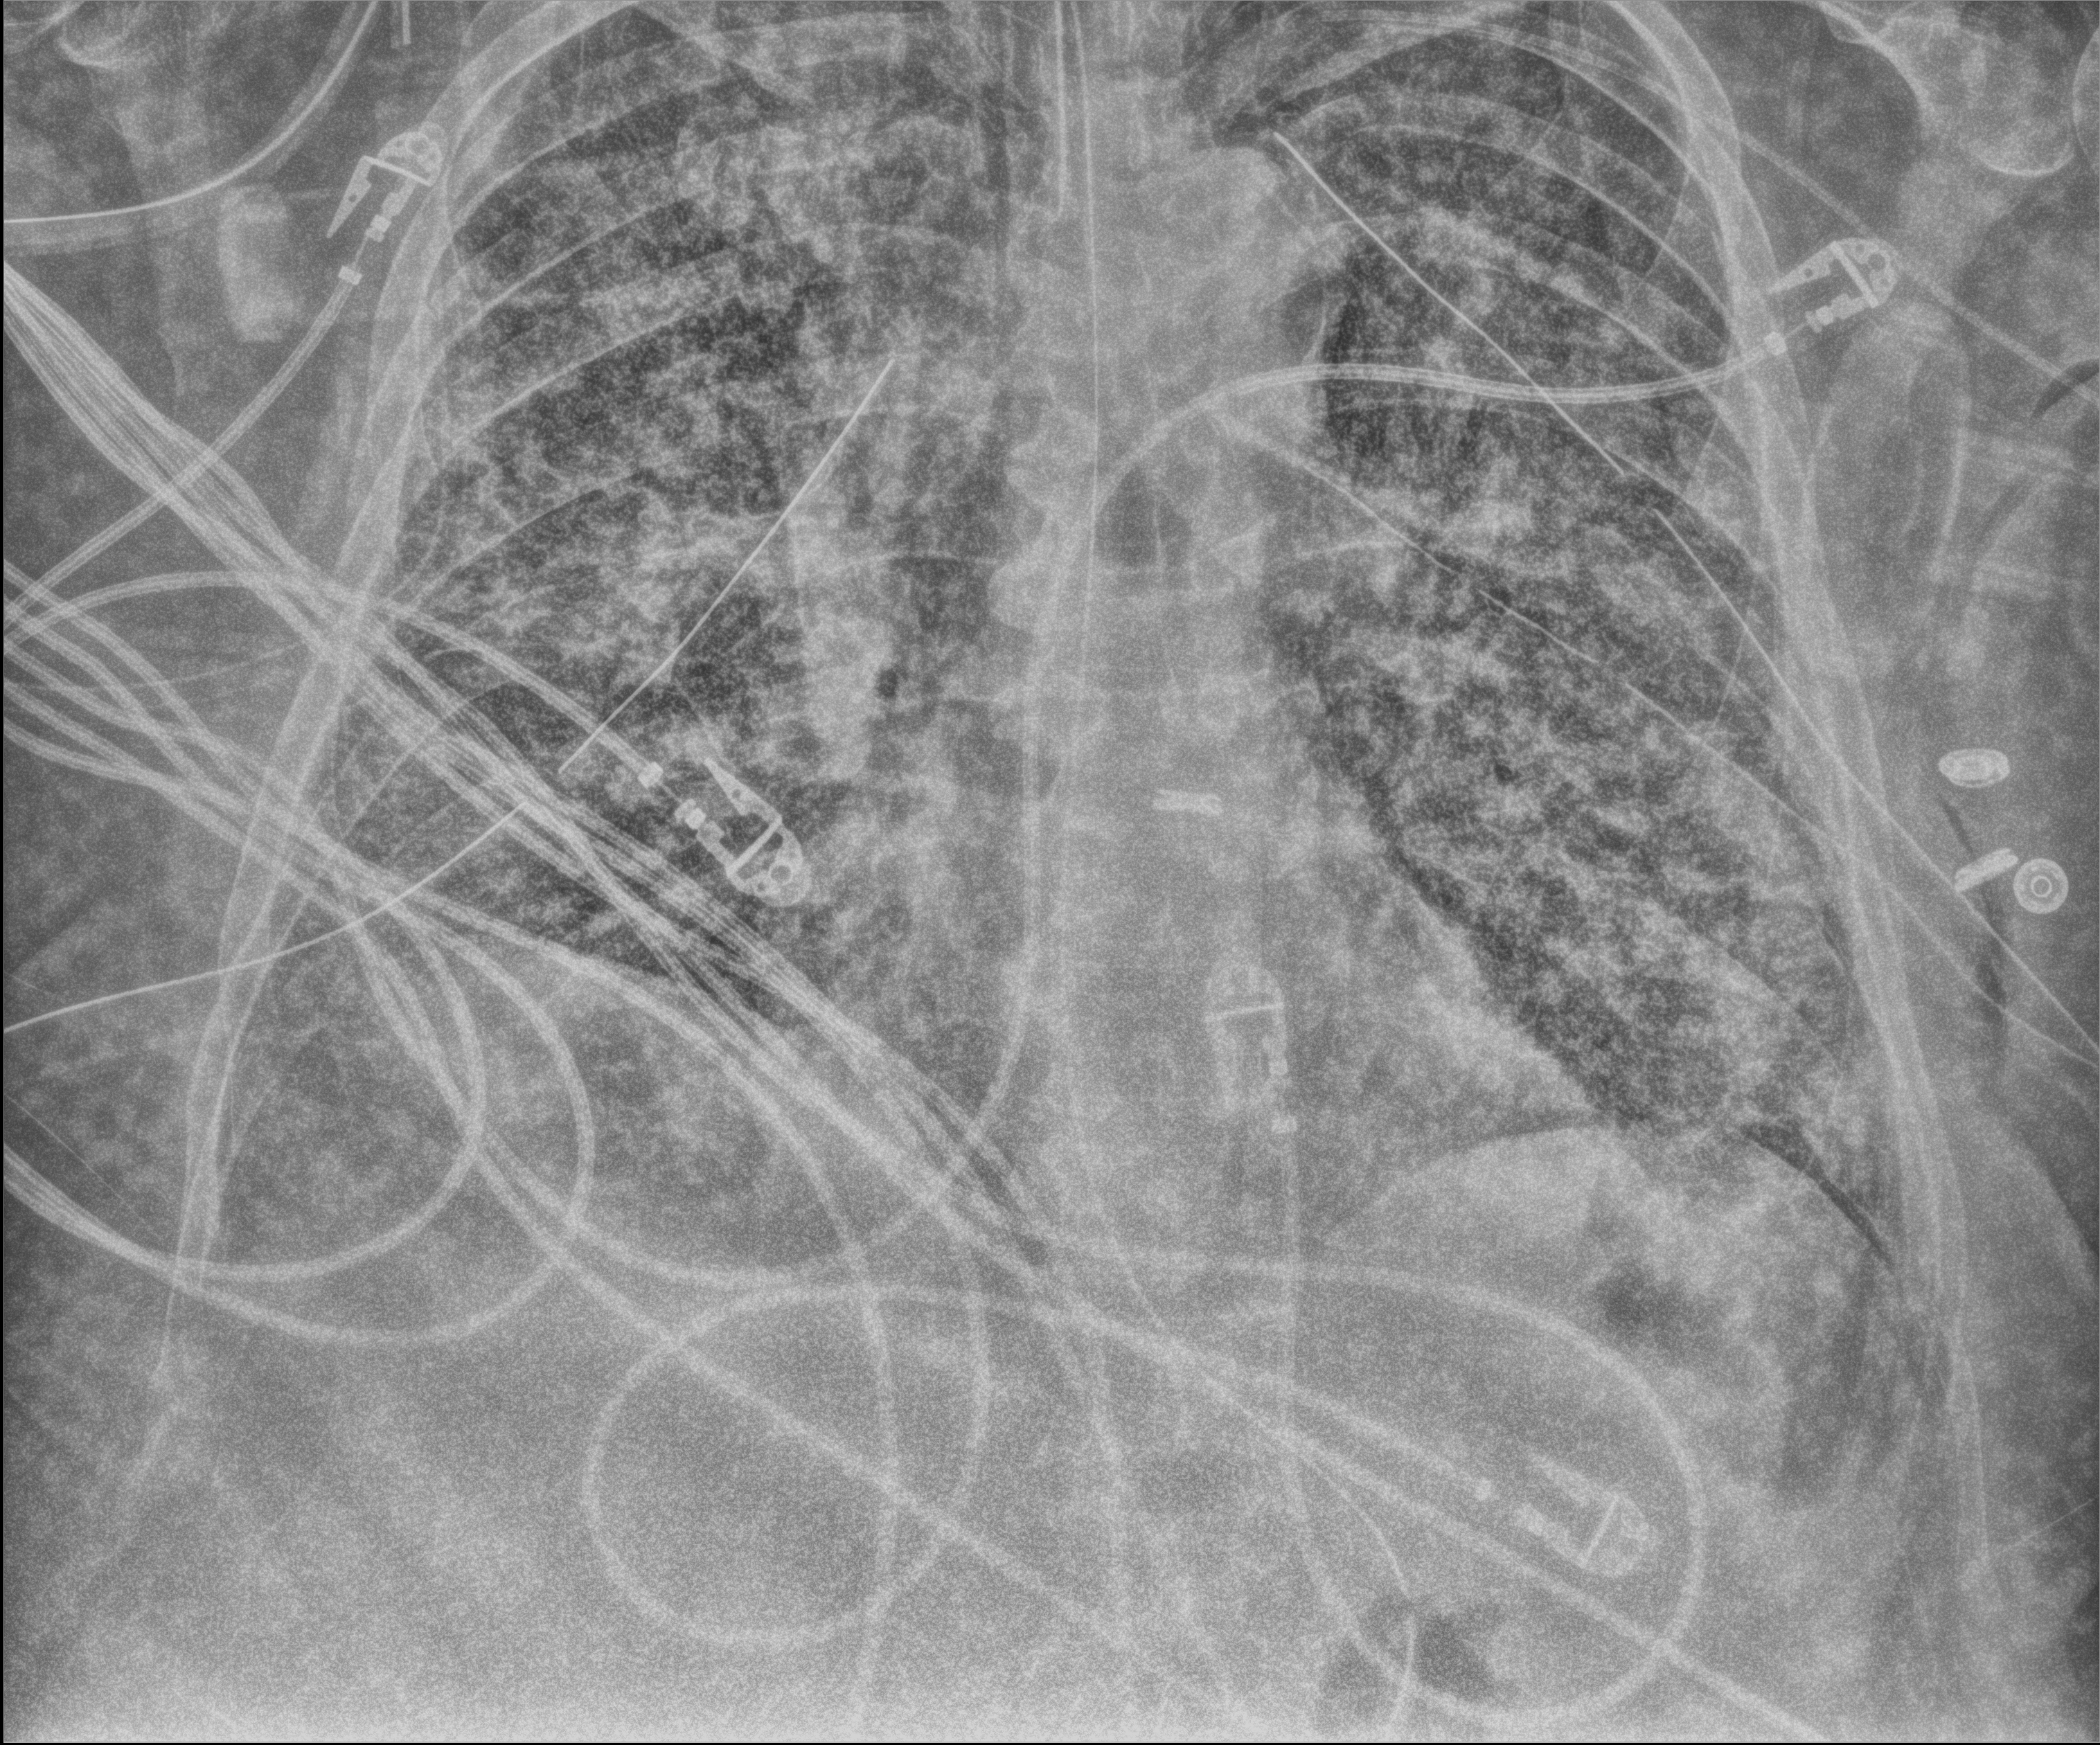
Portable chest radiograph, anteroposterior (AP) projection. Adult patient hospitalised with COVID-19, age 18–59 years.
From the hospital-stay record, not from the radiograph (when in the stay this image was taken is not recorded): length of hospital stay: 28 days.